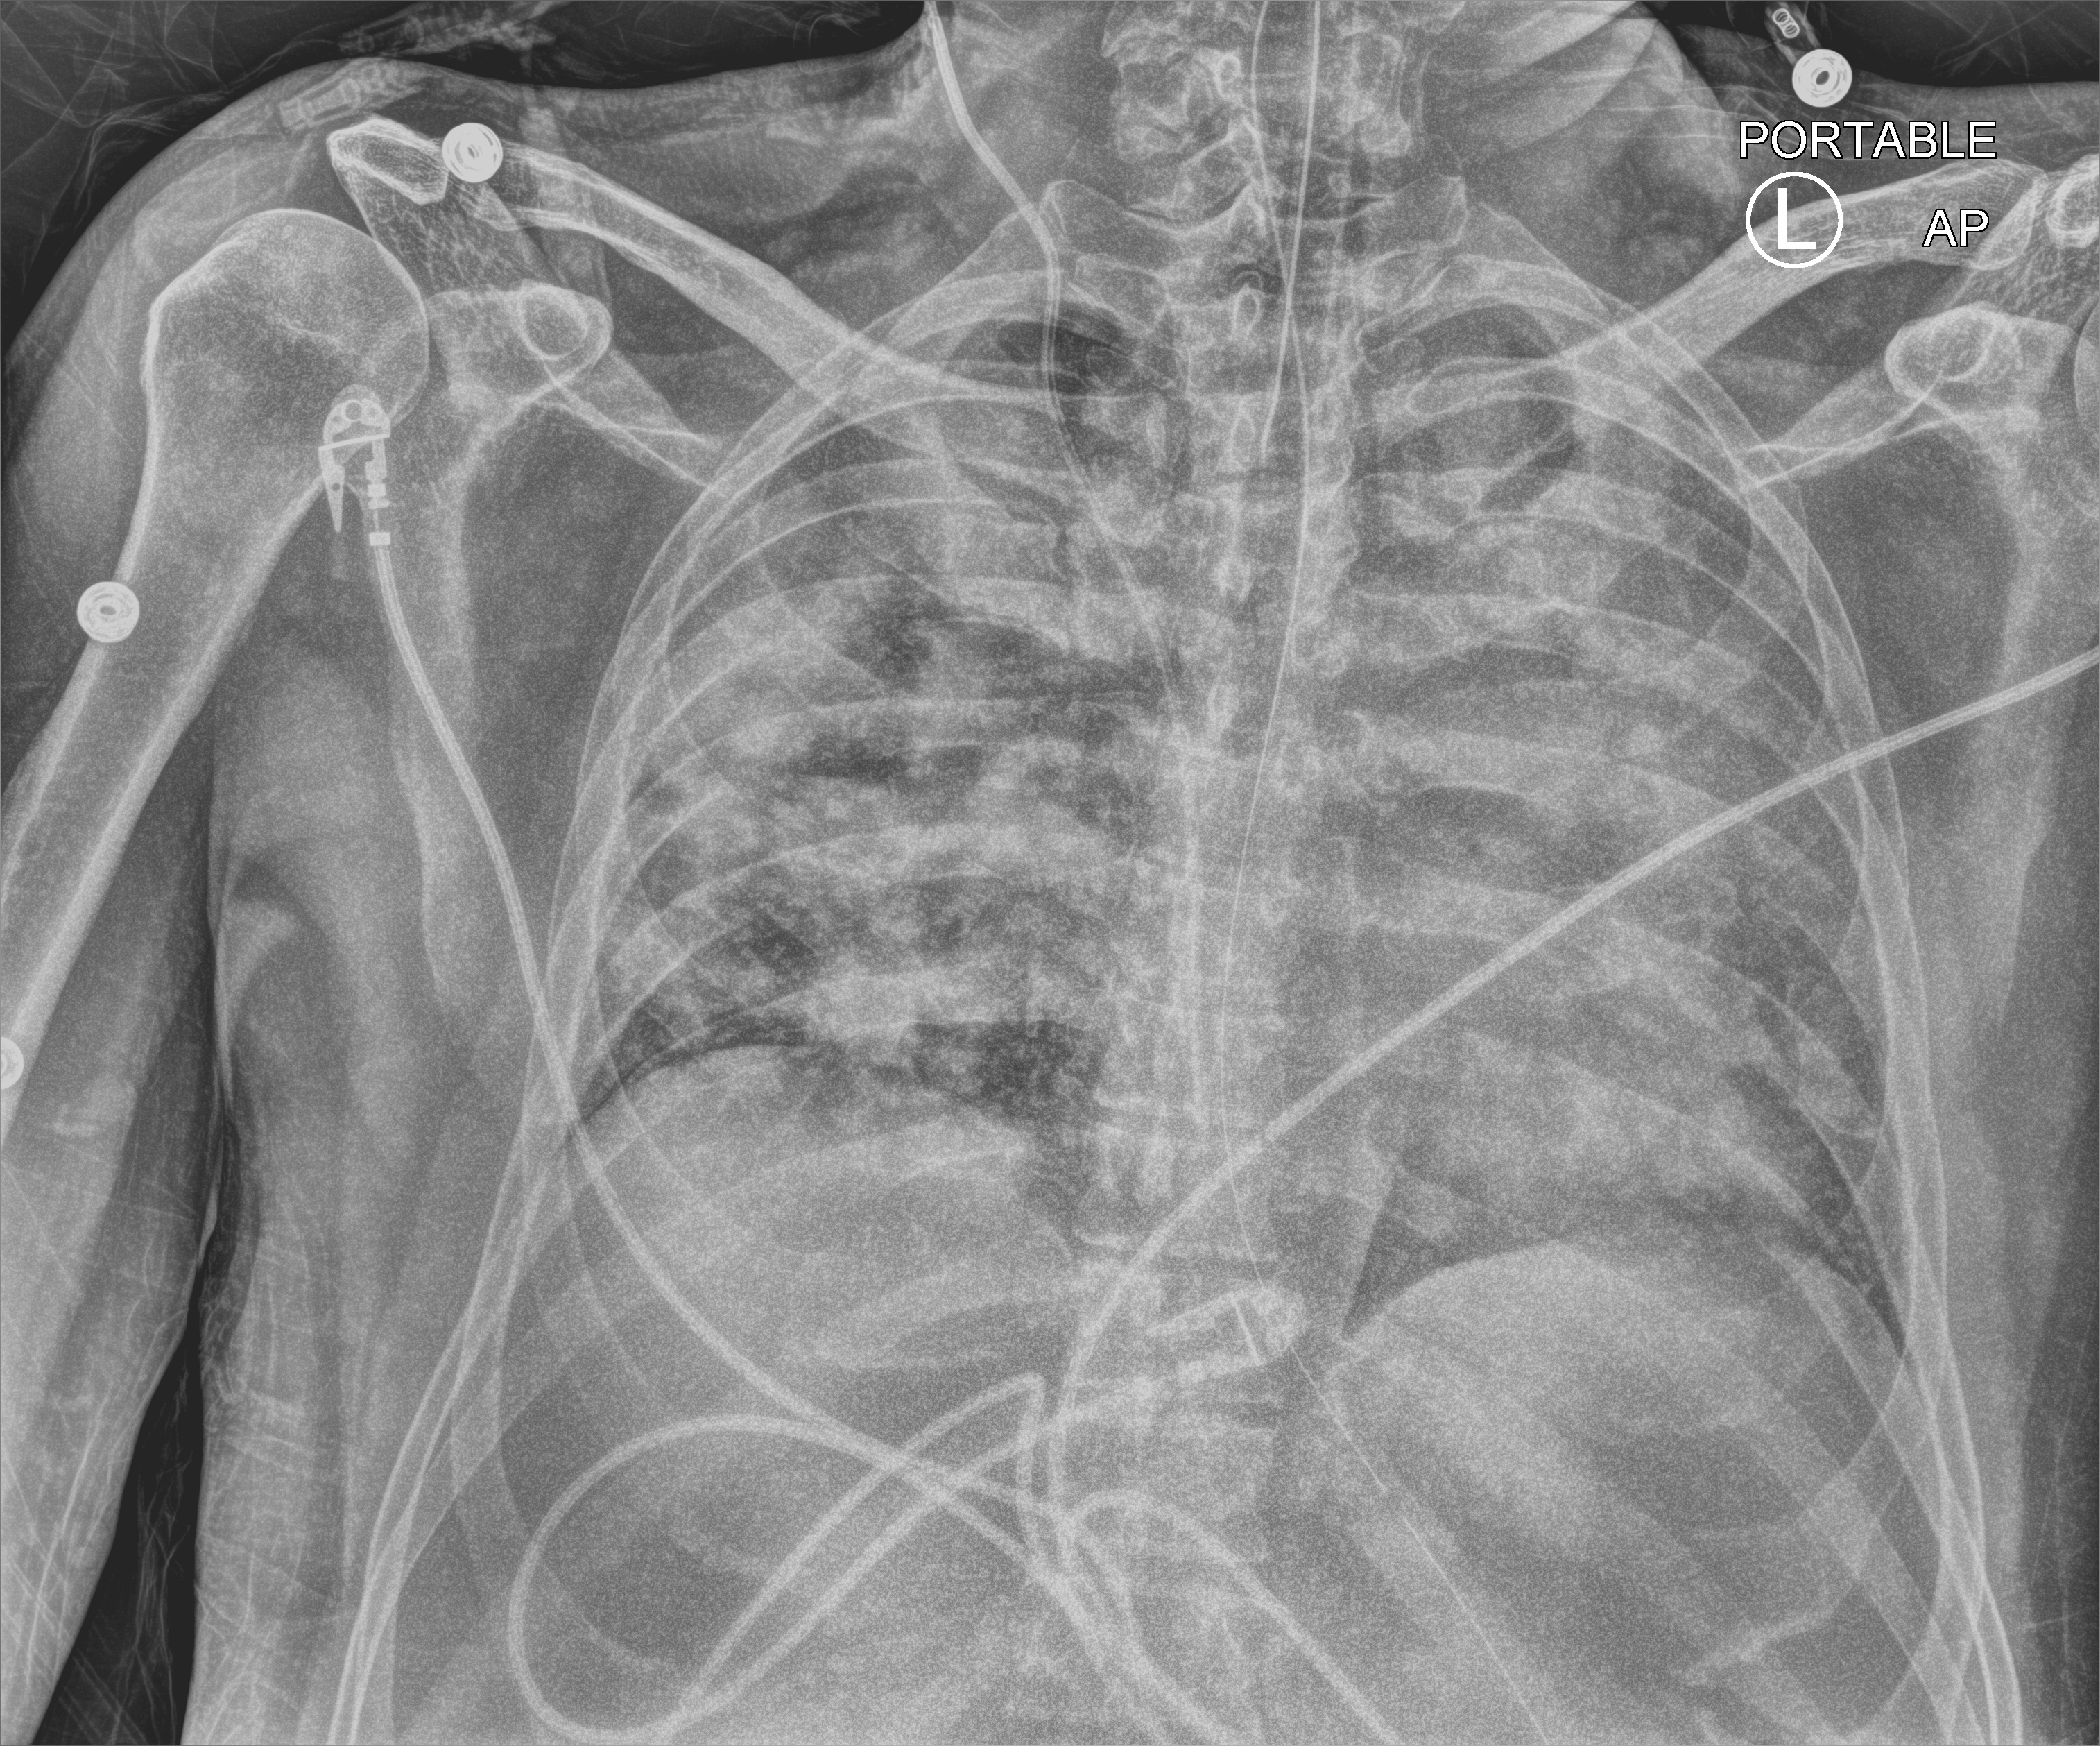
Portable chest radiograph, anteroposterior (AP) projection. Patient hospitalised with COVID-19; male, aged 18–59 years.
Hospital-stay facts (about this admission, not read from this image; timing relative to this image not recorded): diabetes (admission record): no.